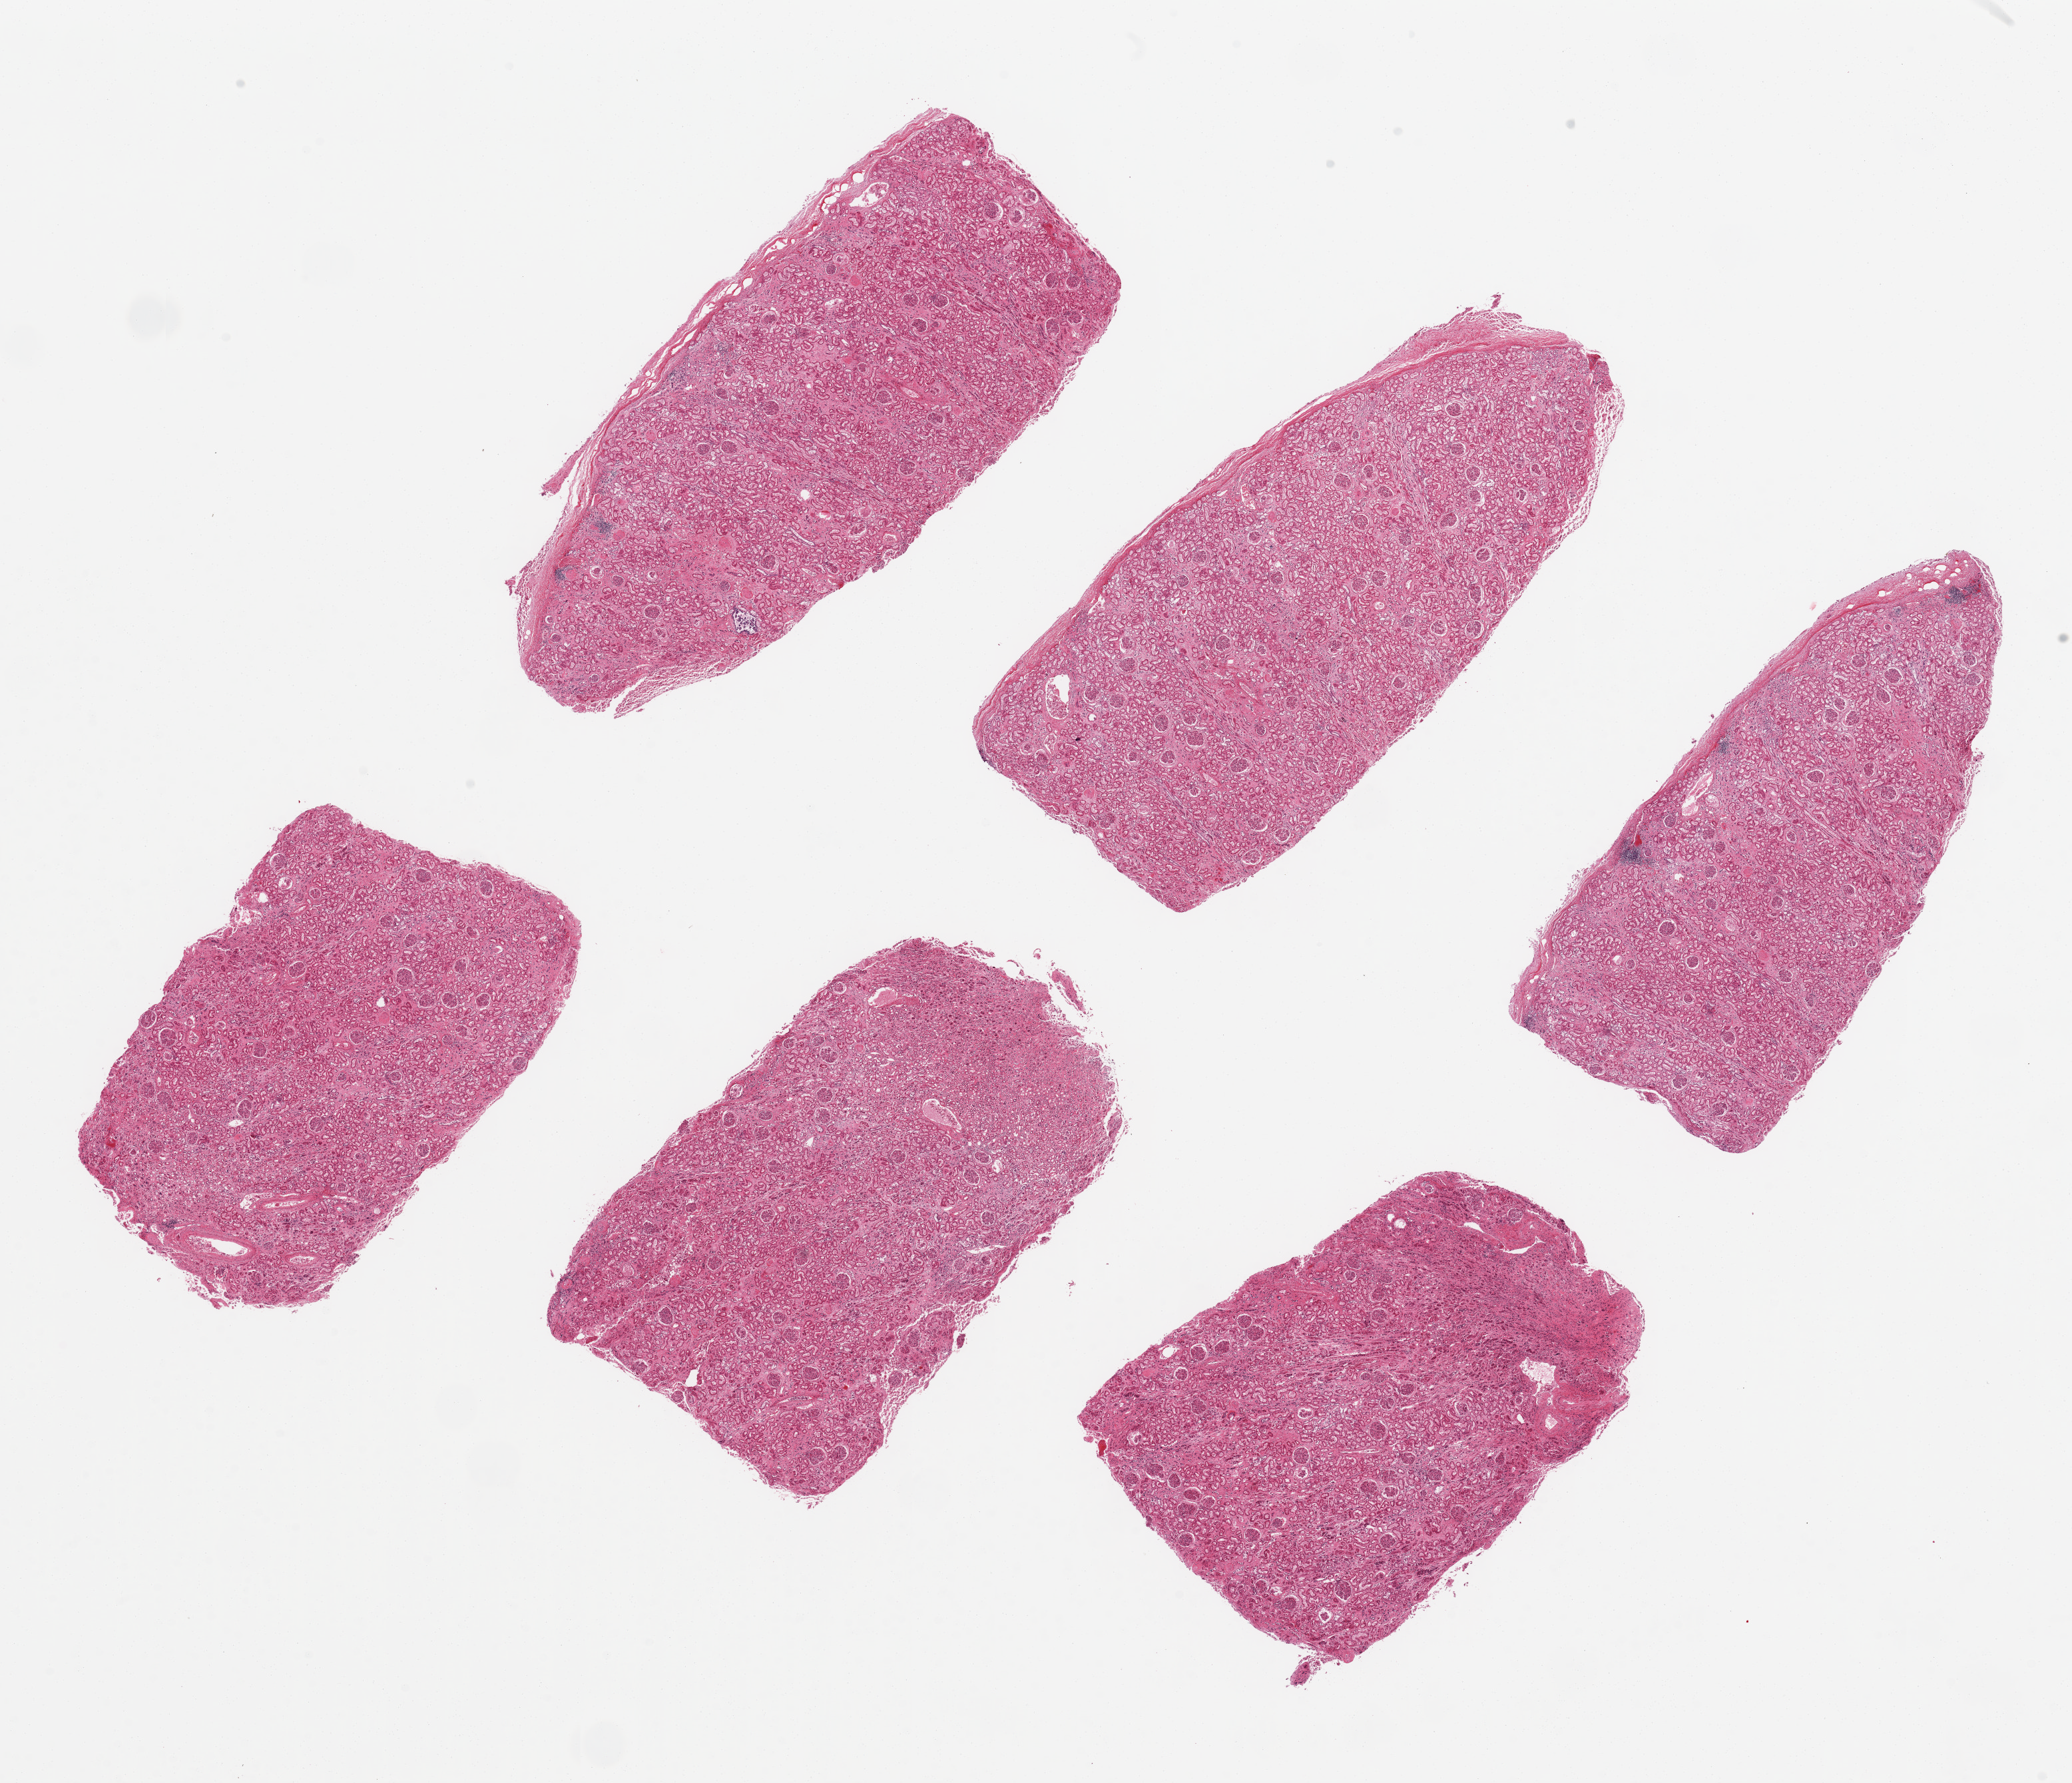
Haematoxylin and eosin whole-slide image, low-resolution overview of the scanned area, about 24.6 x 21.2 mm (slide scanned at 20x); PAXgene-fixed, paraffin-embedded tissue; section of renal cortex (target tissue); donor tissue sample. Donor: male.
Reviewer comment on this tissue sample: 6 pieces, up to 8x4 mm; moderate interstitial fibrosis.